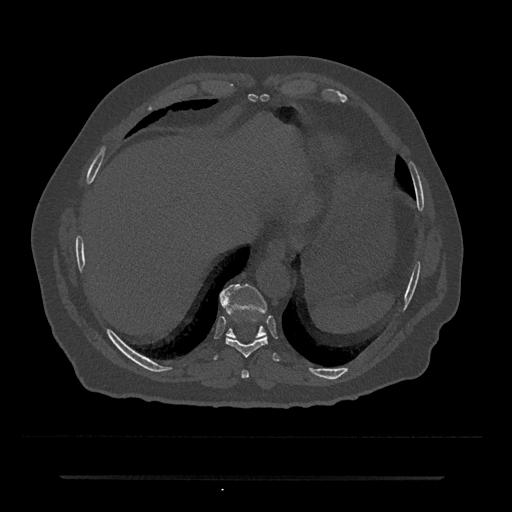
CT including the spine, one axial slice. Position 264 of 797 along the scan axis. Bone window (W 1800 / L 400 HU). 0.5 mm slice thickness. 512 × 512 image matrix, field of view 437 × 437 mm. Male patient, age 69 years. From the clinical record (not read from this slice): primary cancer: prostate.
Annotated regions visible in this slice (semi-automatically segmented with operator editing):
- T10 vertebra: bounding box [x1, y1, x2, y2] px = [220, 283, 267, 339]
- T8 vertebra: [241, 370, 249, 379]
- T9 vertebra: [212, 336, 279, 361]